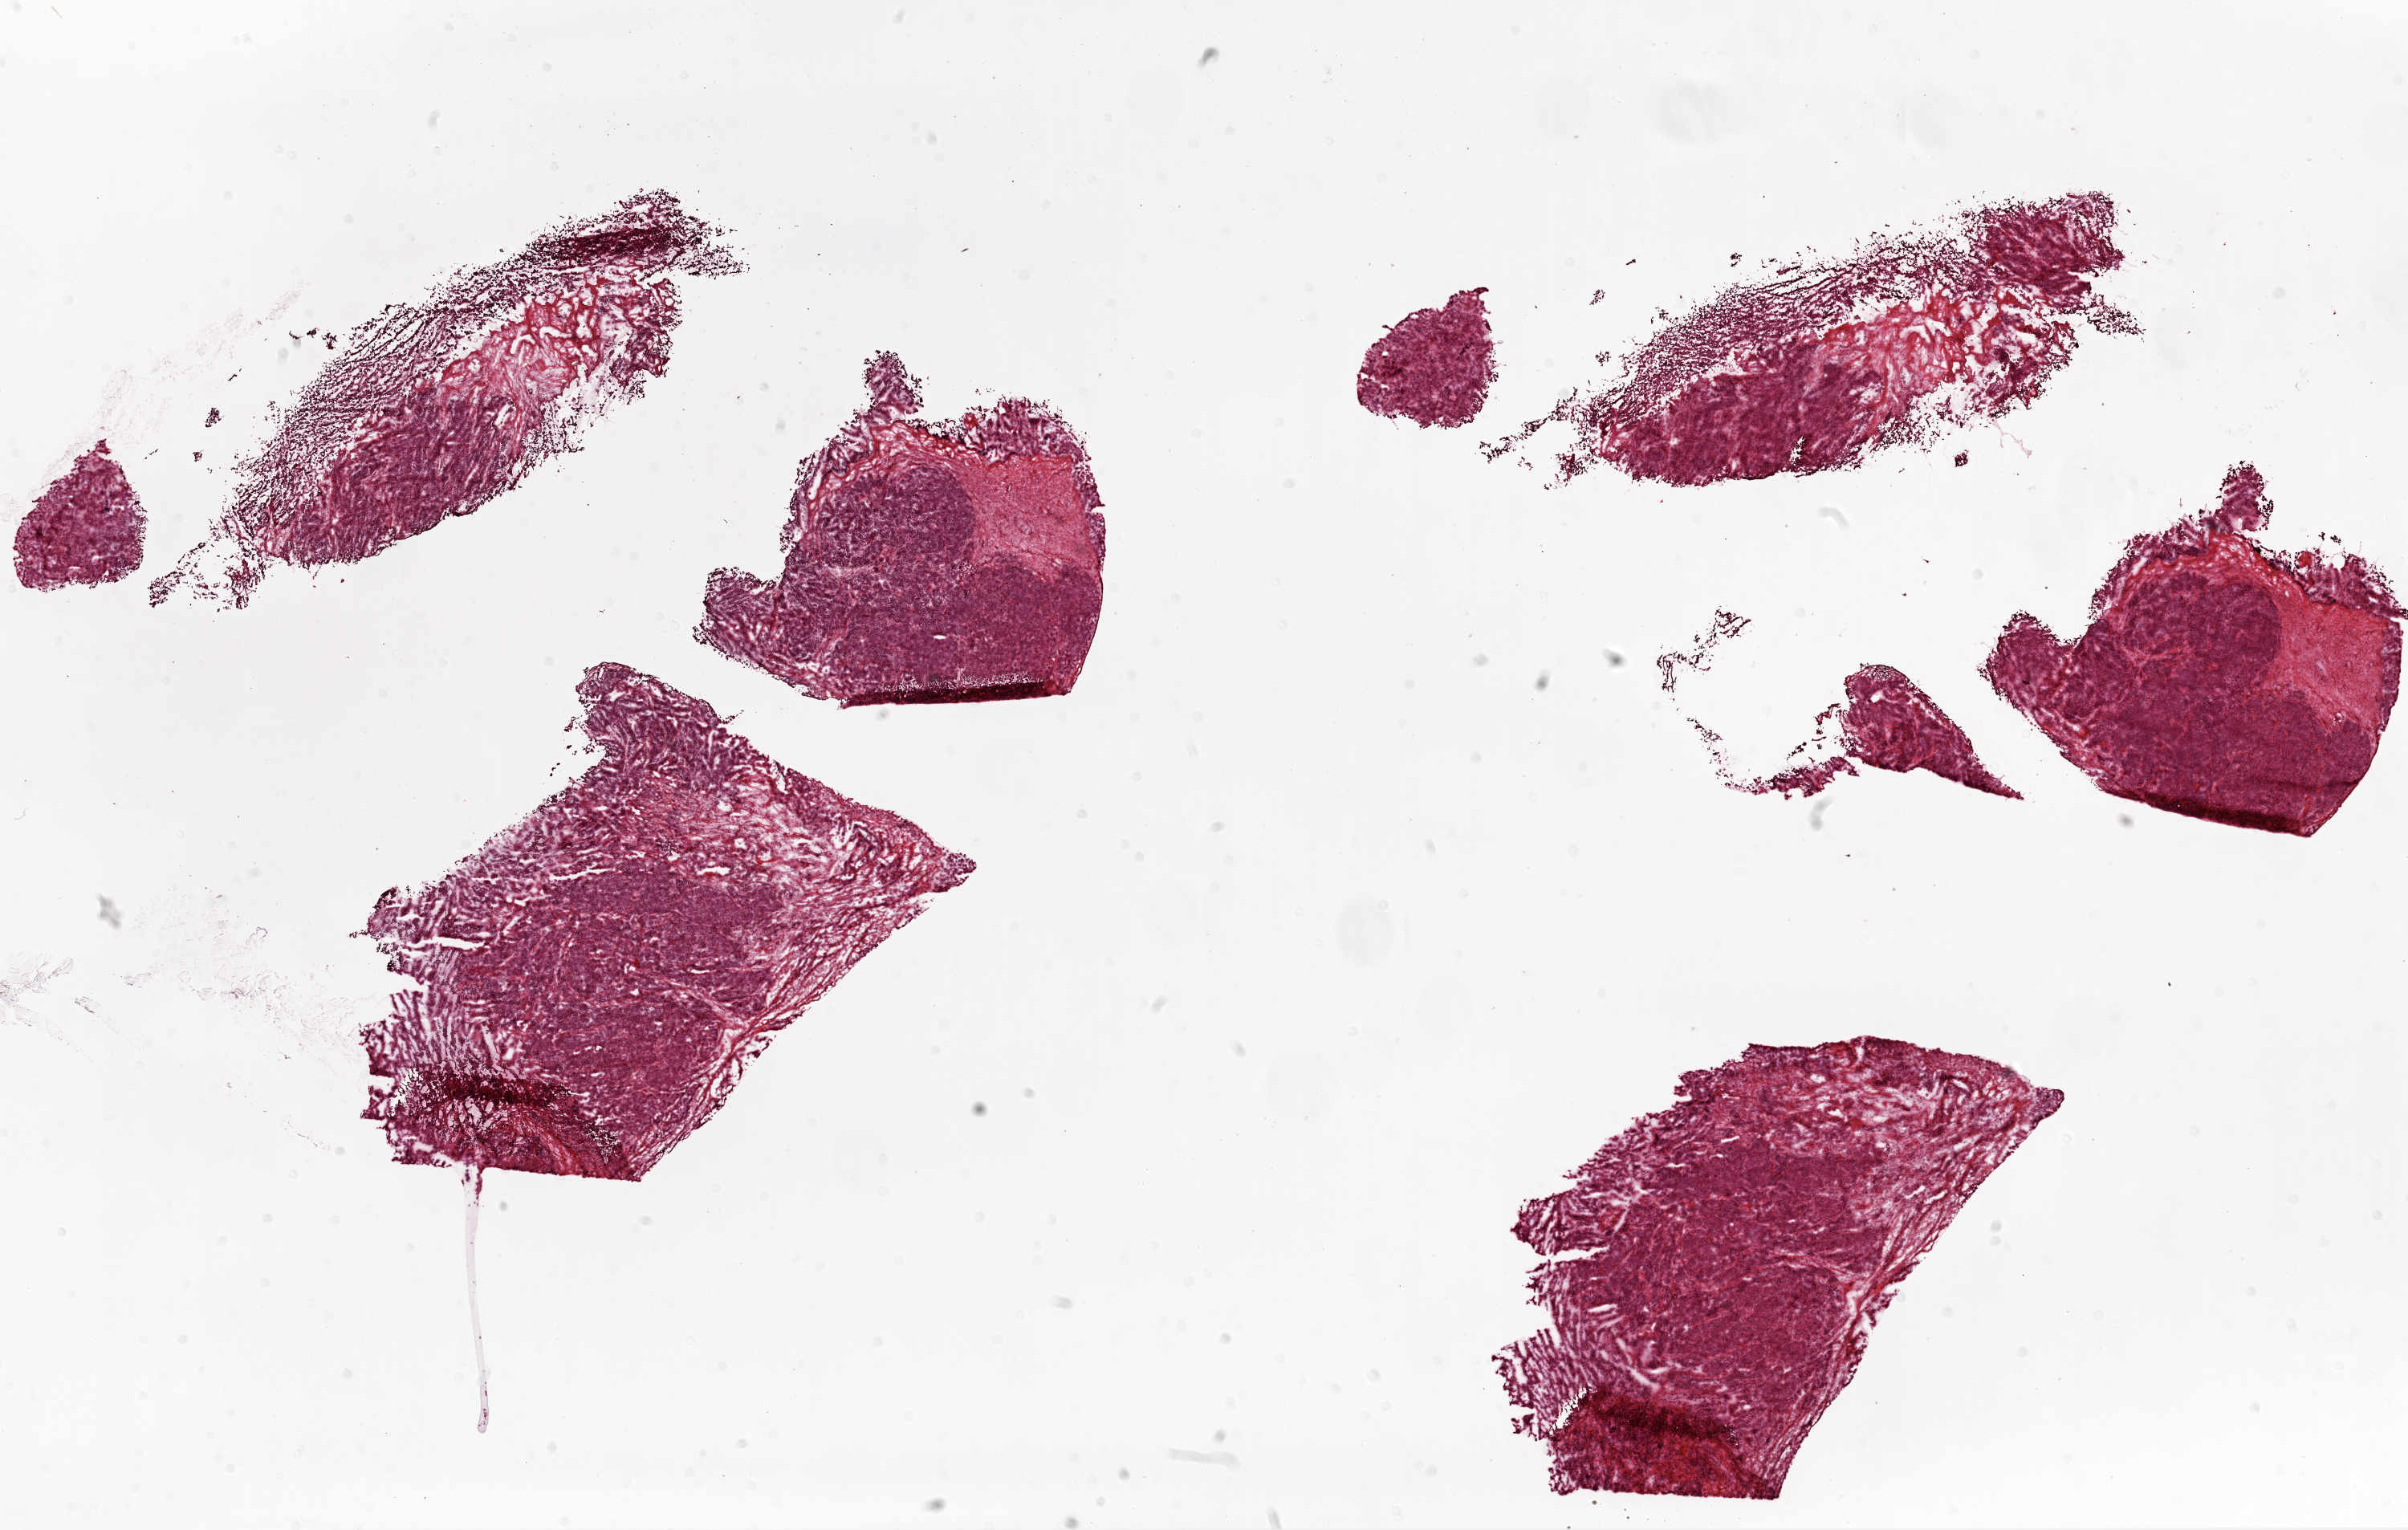
Hematoxylin and eosin (H&E) stained whole-slide image, low-resolution overview of the scanned area, about 24.1 x 15.3 mm (acquisition: 20x scan), frozen section from the top of the tissue portion, sample: primary tumour, ovary. Patient: female, age at initial diagnosis 66 years. Histologic grade: G3 (poorly differentiated). Pathologist review of this section (percent, as recorded): tumour cells 75%, tumour nuclei 75%, normal cells 0%, stromal cells 25%, necrosis 0%. Inflammatory infiltration, as recorded: lymphocyte infiltration 0%, monocyte infiltration 0%, neutrophil infiltration 0%.
FIGO stage: IIIC. Histologic diagnosis: Serous cystadenocarcinoma, NOS.